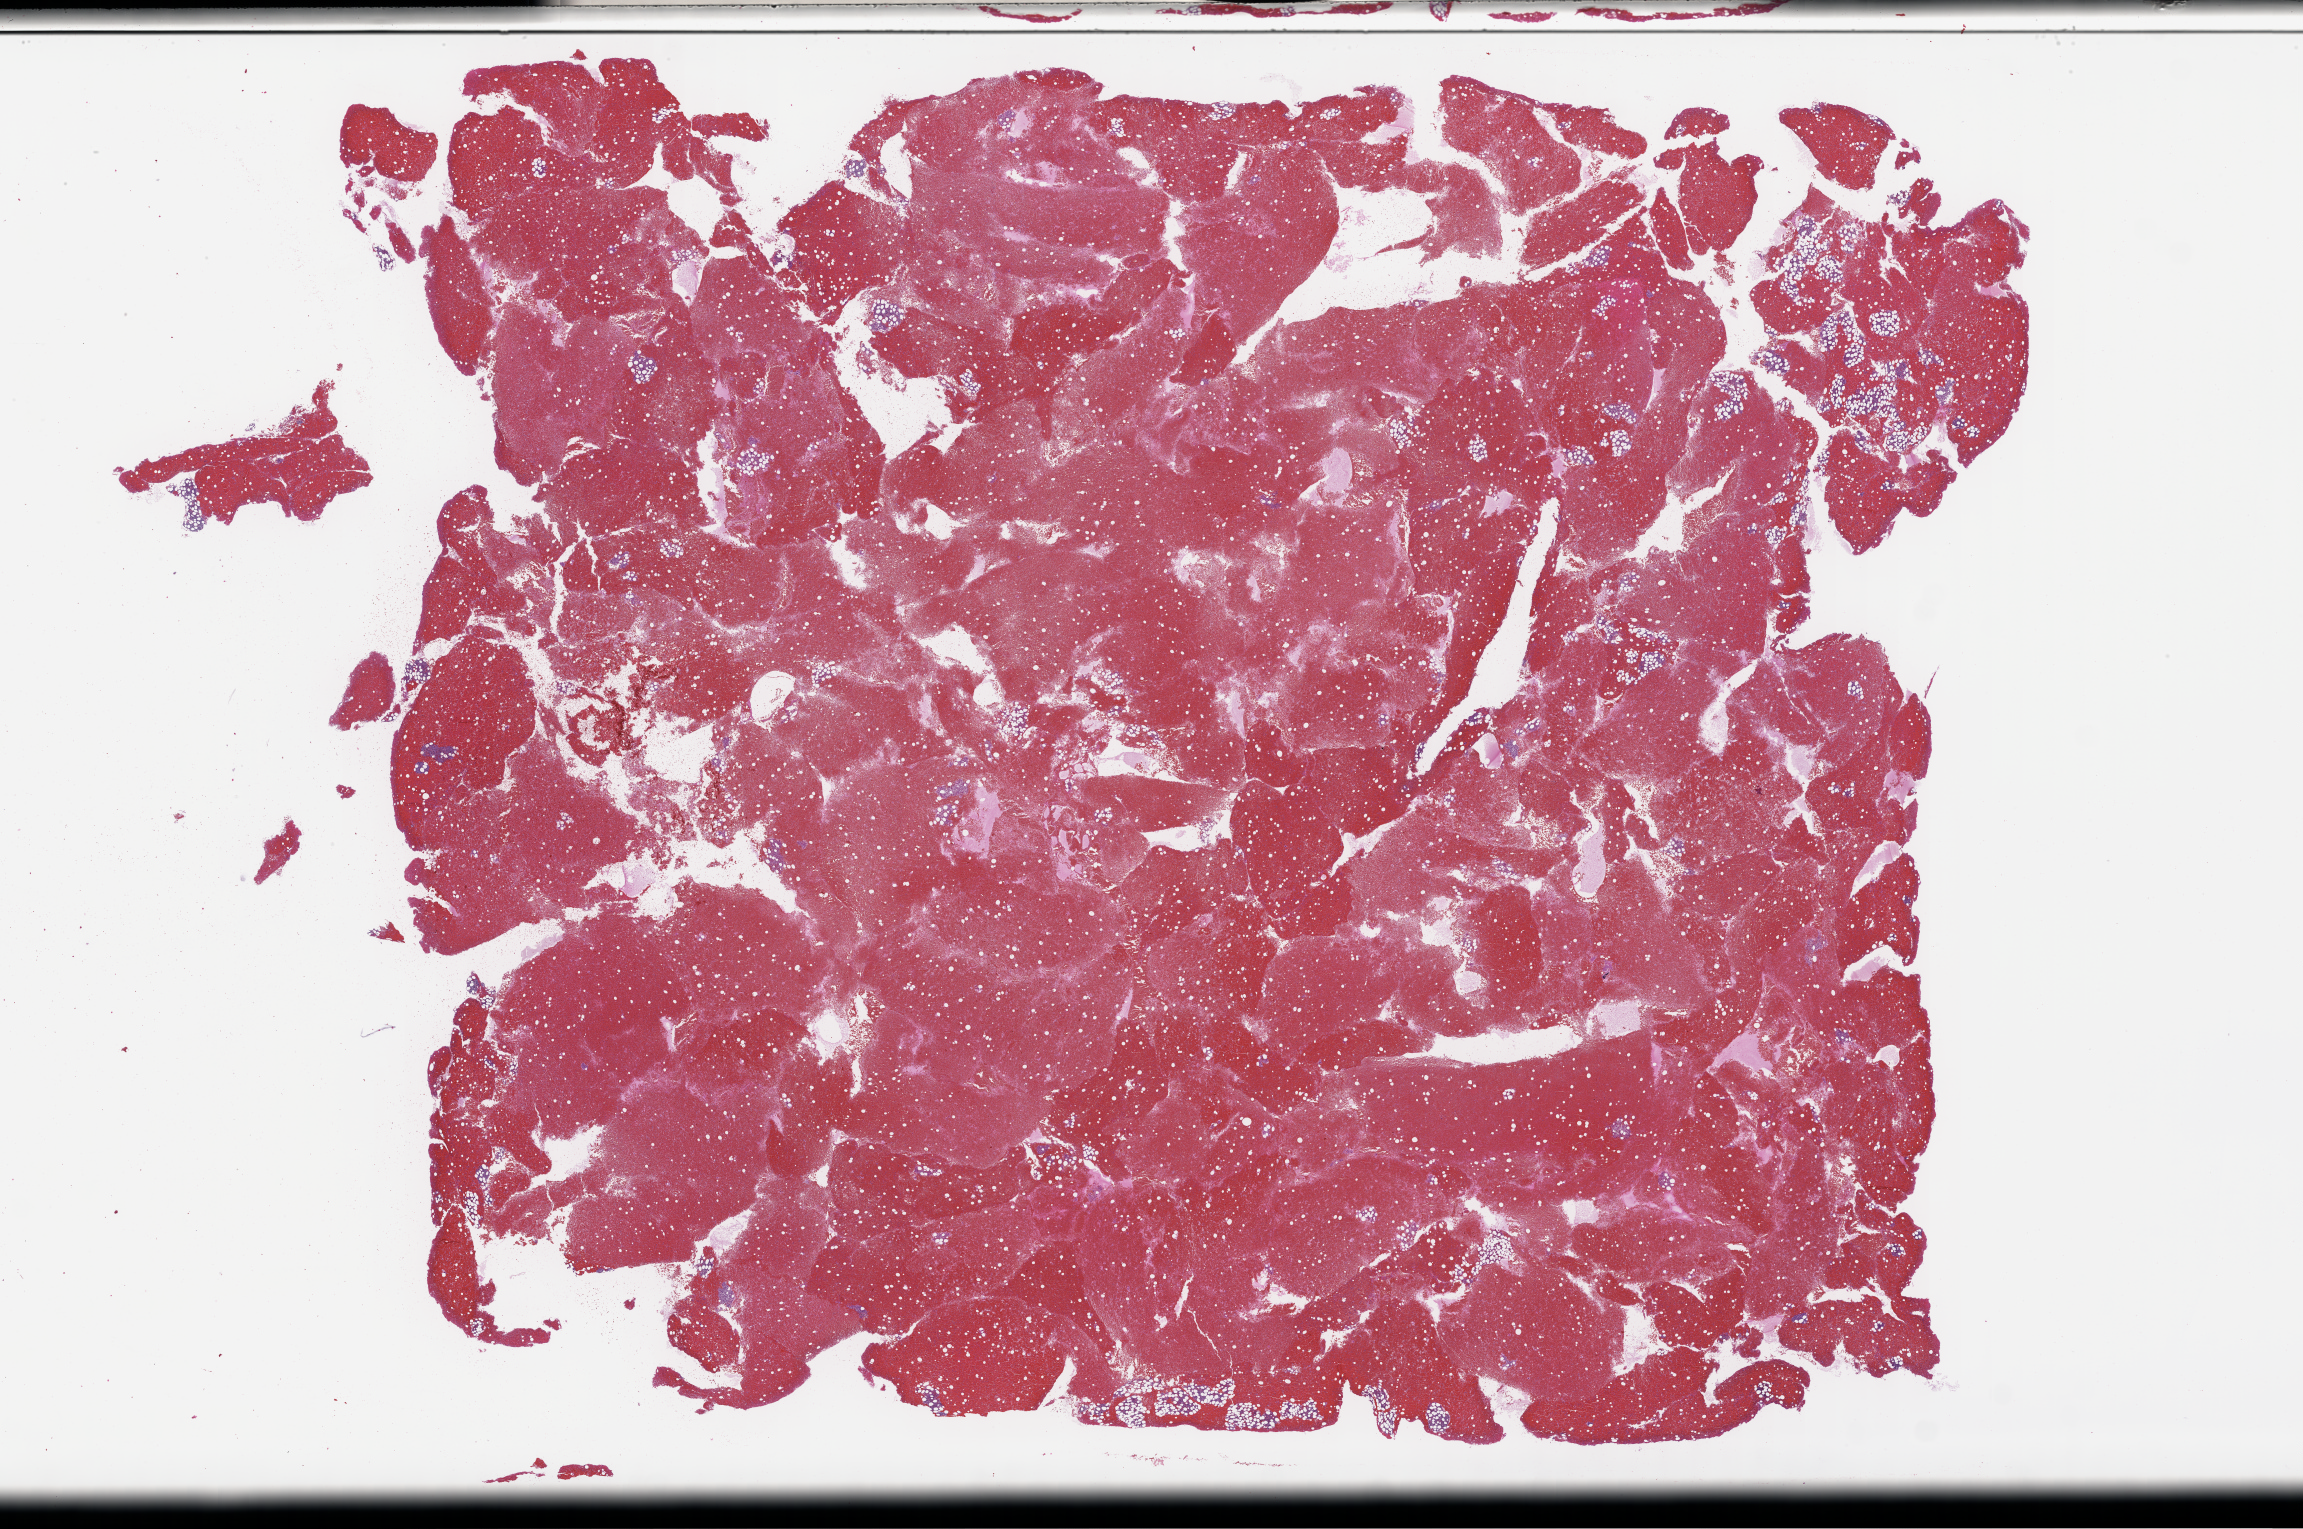
Digitized haematoxylin and eosin-stained section, whole scanned area (about 37.2 x 24.7 mm) shown as a low-resolution overview; FFPE section; site: bone marrow; specimen time point: collected at disease progression. Patient: female.
* this section: primary tumour tissue
* diagnosis: Plasma Cell Myeloma